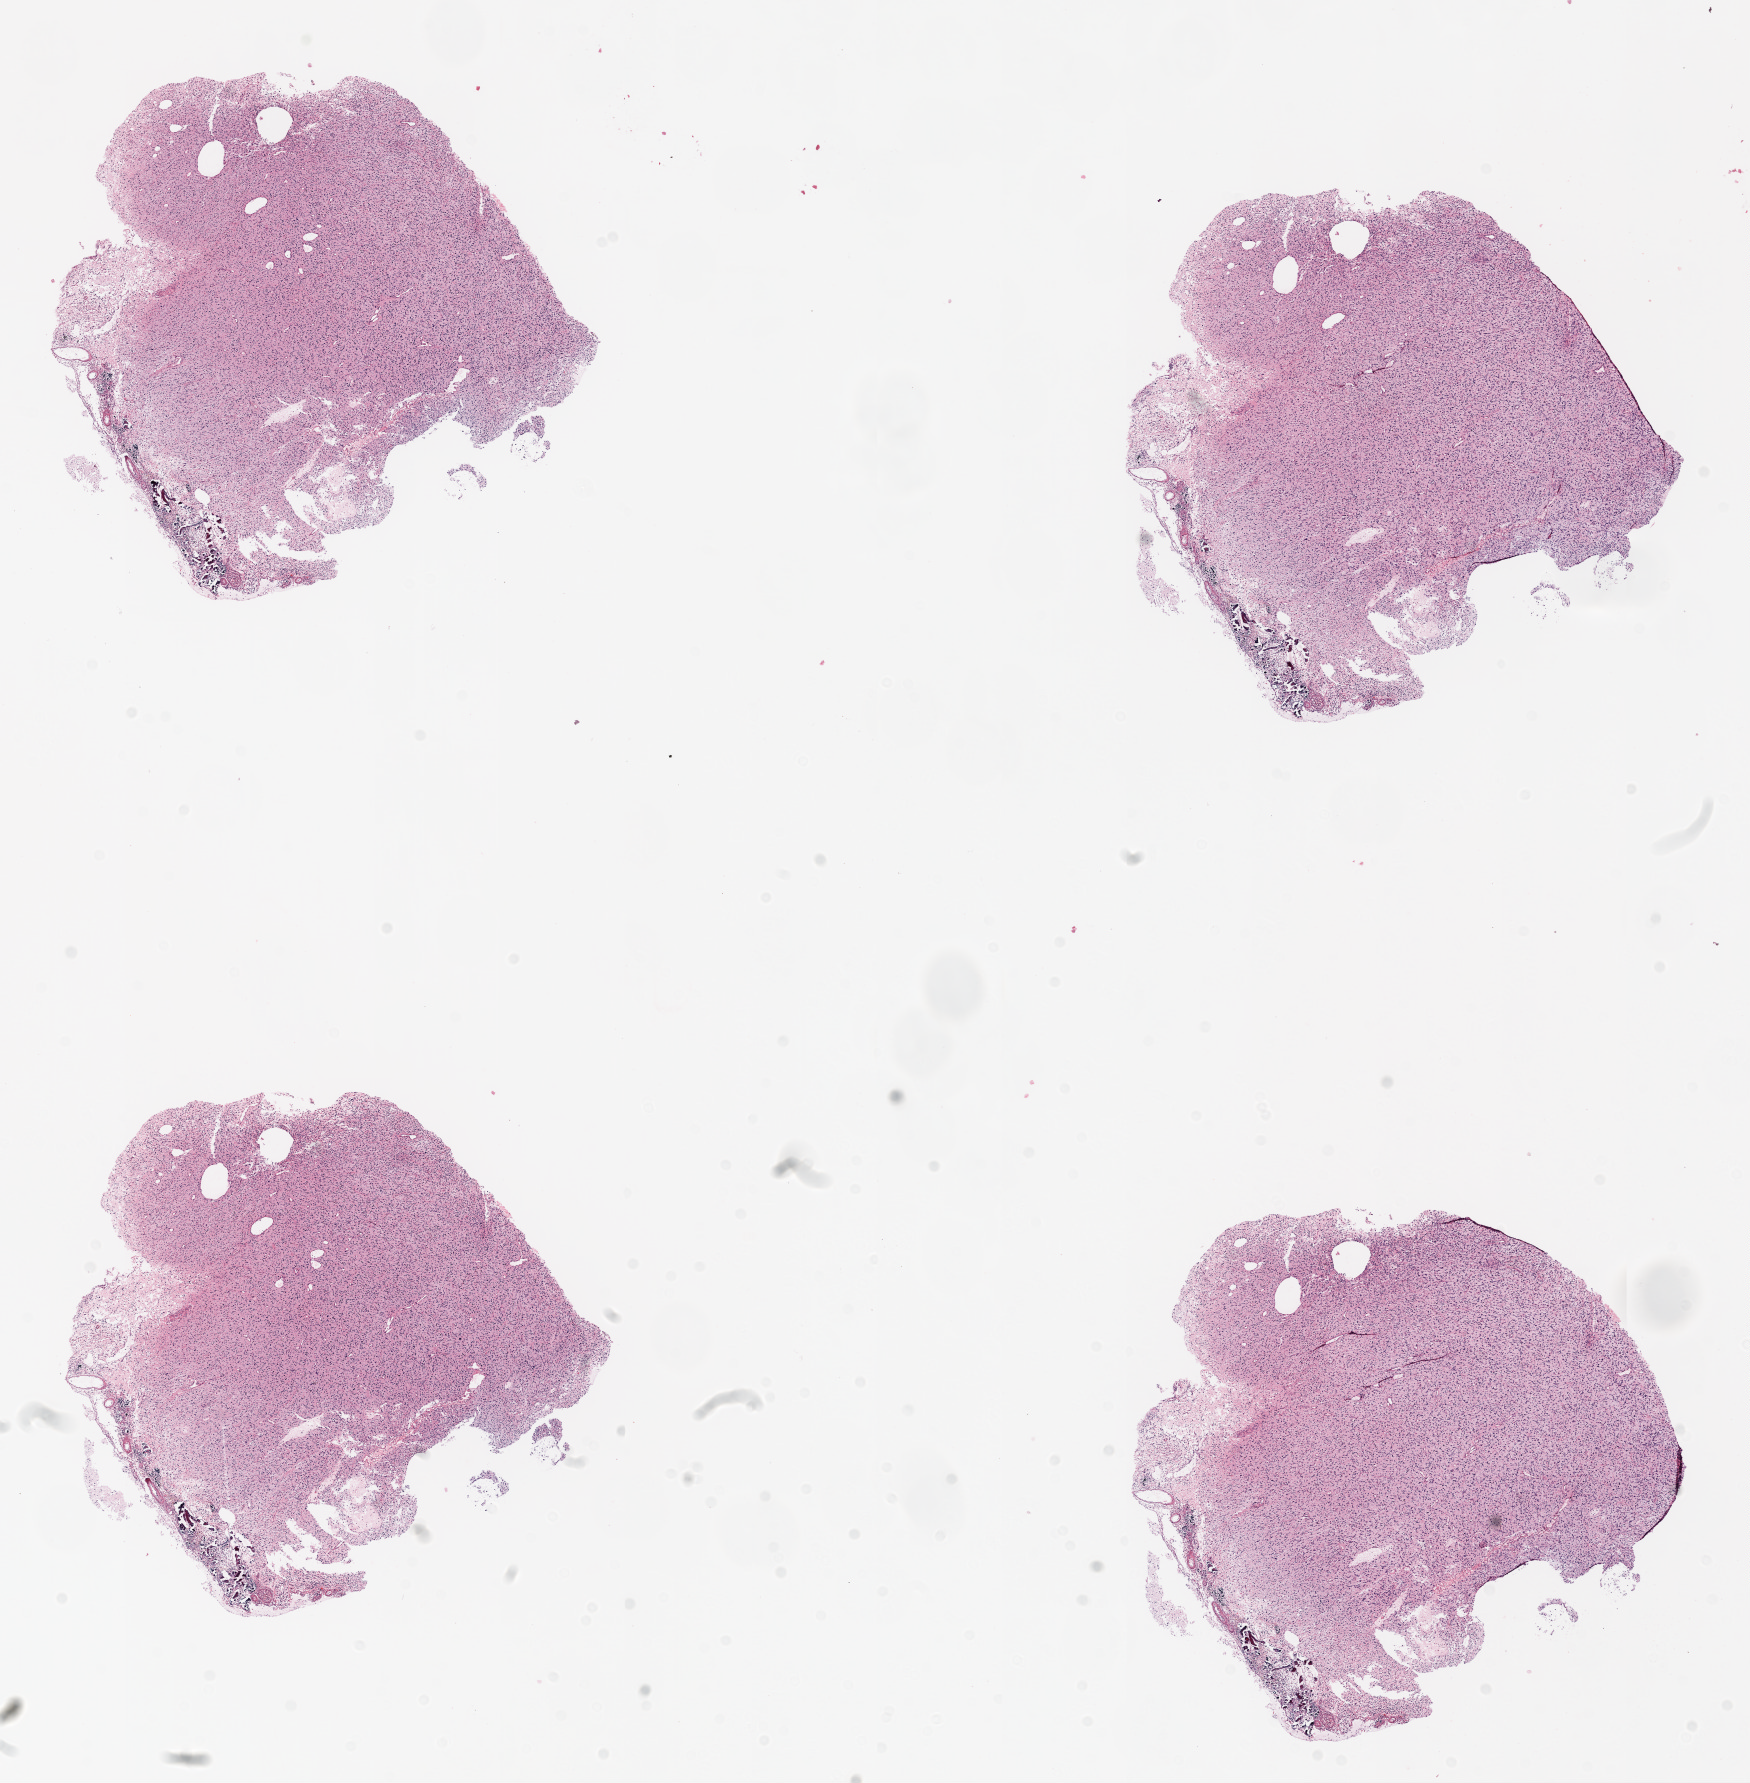
Digitized H&E-stained tissue section (whole slide), low-resolution overview of the scanned area, about 14.0 x 14.3 mm (slide scanned at 20x); formalin-fixed paraffin-embedded (FFPE) diagnostic section; brain, primary tumour sample. Patient: female, age at initial diagnosis 28 years.
• histologic diagnosis: Glioblastoma